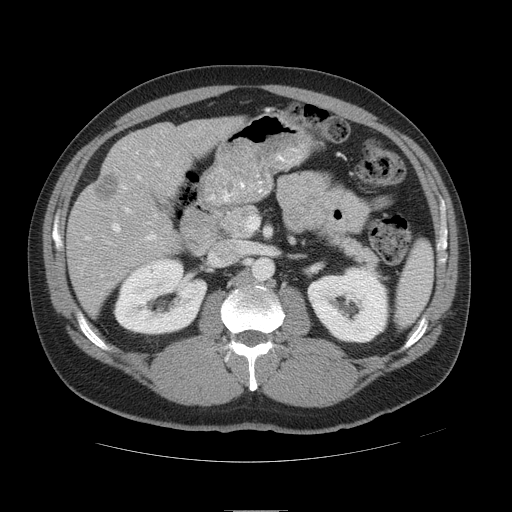
Contrast-enhanced abdominal CT, one axial slice. Reconstruction kernel STANDARD. Intravenous contrast given. Soft-tissue window (W 400 / L 40 HU). 5 mm slice thickness. 512 × 512 image matrix, field of view 425 × 425 mm. Male patient, age 52 years. Case-level facts recorded for this patient, not image findings: diagnosis: colorectal cancer liver metastases, imaged before liver resection; multiple liver metastases: yes; largest metastasis: 5.1 cm.
Outlined on this slice (manually delineated by an expert):
- hepatic veins: bounding box (x1, y1, x2, y2) in pixels: (112, 153, 152, 233)
- liver: (69, 118, 238, 309)
- planned liver remnant (the part of the liver to remain after resection): (132, 118, 239, 182)
- portal vein (with intrahepatic branches): (107, 169, 158, 244)
- liver metastasis: (95, 176, 119, 202)